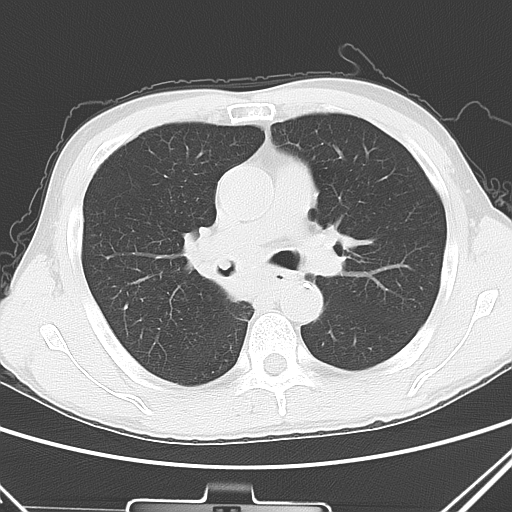
Chest CT, one axial slice; slice 29 of 51 in the series (ordered by position); lung window (W 1500 / L -600 HU); 512 × 512 image matrix. Male patient, age 52 years. Case-level facts recorded for this patient, not image findings: clinical TNM (as recorded): T2a N0 M1c.
Structures marked on this image (bounding box drawn by a radiologist):
- lung tumour (recorded histology: squamous cell carcinoma): box from (x=181, y=211) to (x=246, y=318) px